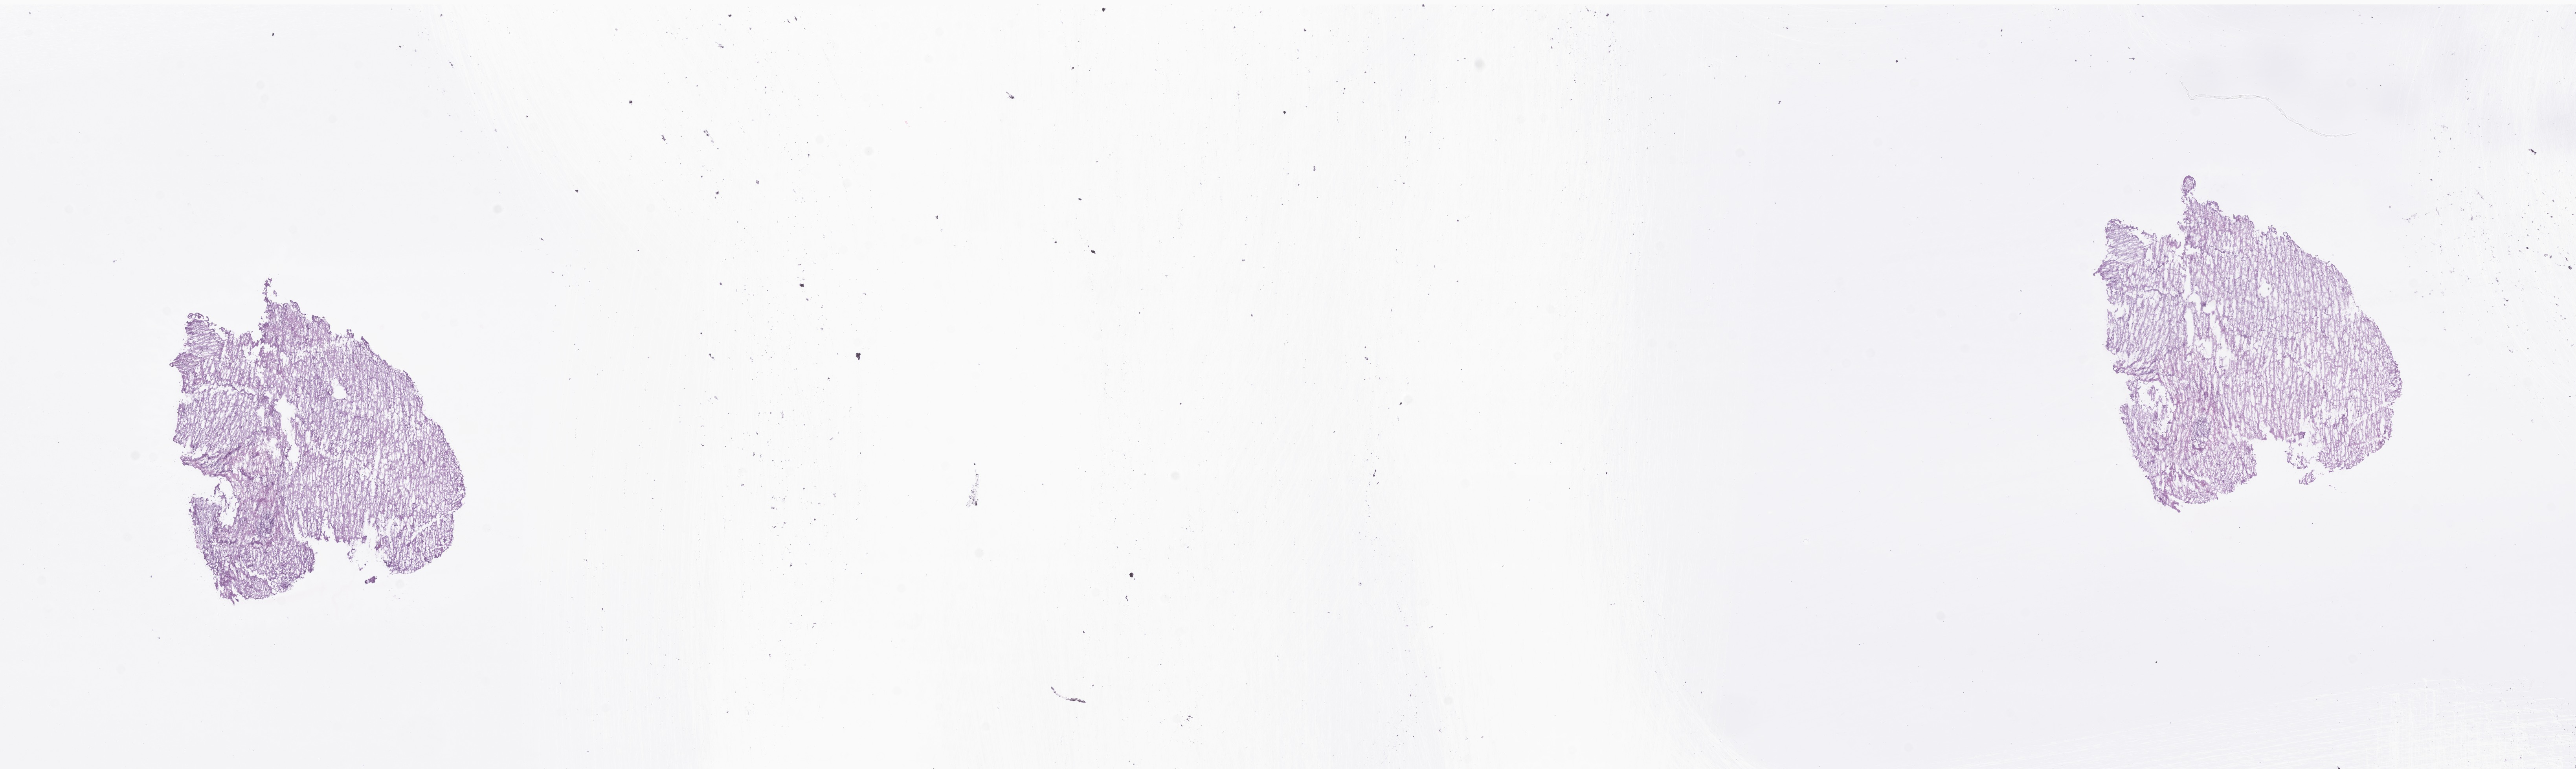
Digitized H&E-stained section of tumor tissue from the orbit, shown as a low-resolution overview of the whole scanned area (about 27.6 x 8.2 mm), frozen section. Female patient, age 145 days.
Diagnosis: Ganglioglioma, NOS.